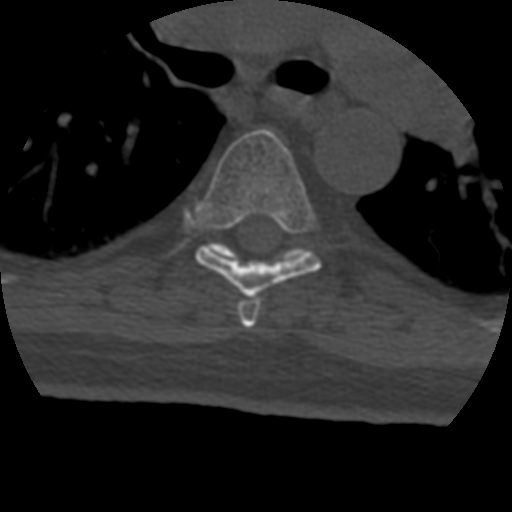
CT including the spine, one axial slice; position 298 of 399 along the scan axis; reconstruction kernel STANDARD; bone window (W 1800 / L 400 HU); 1.25 mm slice thickness; 512 × 512 image matrix, field of view 160 × 160 mm. Patient age 69 years. Case-level facts recorded for this patient, not image findings: primary cancer: prostate.
Annotated regions visible in this slice (semi-automatically segmented with operator editing):
- T5 vertebra: bounding box [x1, y1, x2, y2] px = [237, 296, 261, 328]
- T6 vertebra: [193, 129, 321, 297]
- T7 vertebra: [206, 242, 309, 262]